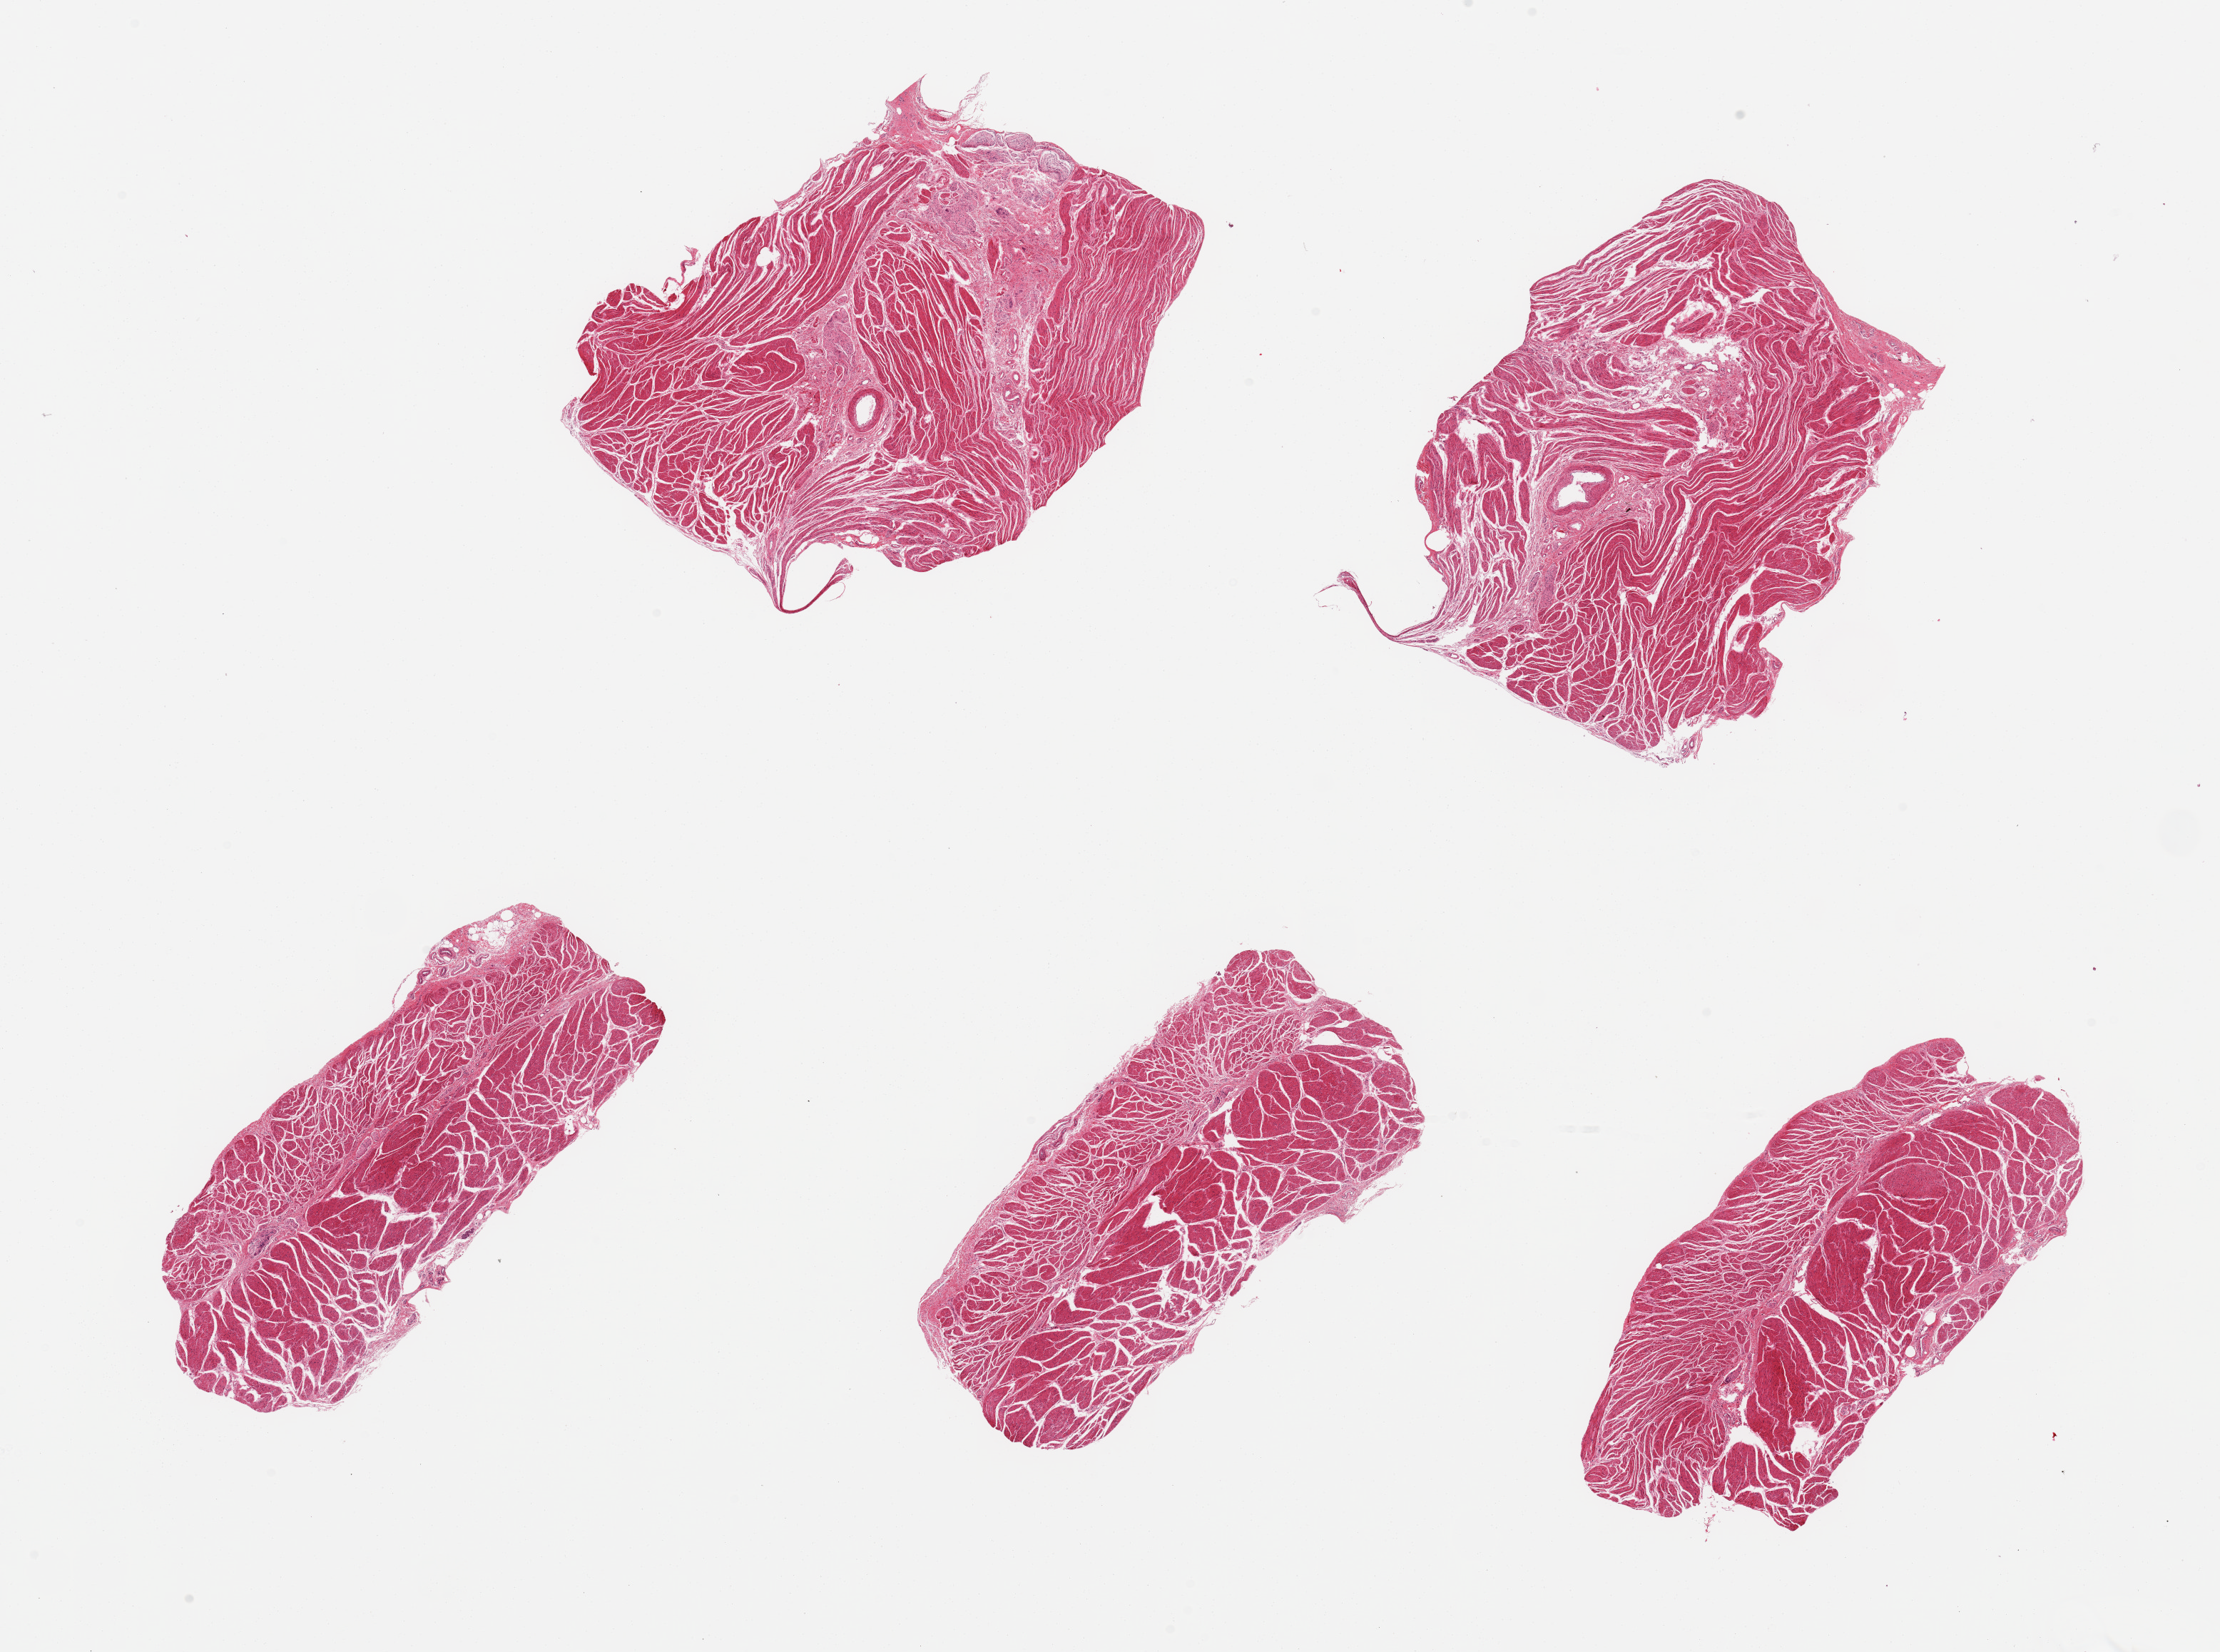
Whole-slide image, hematoxylin and eosin (H&E) stain, low-resolution overview of the scanned area, about 24.6 x 18.3 mm (slide scanned at 20x), PAXgene-fixed, paraffin-embedded tissue, section of gastroesophageal junction (target tissue), donor tissue sample.
Reviewer comment on this tissue sample: 5 pieces; well dissected muscularis.